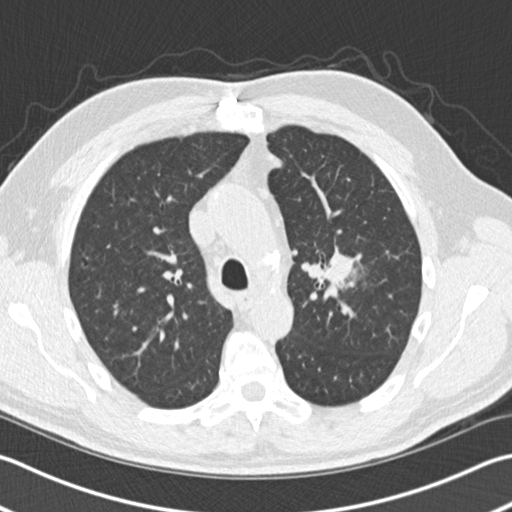
Axial slice from a low-dose chest CT screening exam. Third annual screen. Lung window (W 1500 / L -600 HU). 2 mm slice thickness. Standard (soft-tissue) reconstruction kernel (B30f). Slice 47 of 153 in the series. 512 × 512 image matrix, field of view 346 × 346 mm. Male, age 65 years at enrolment. Former smoker at enrolment.
• Lesion marked by an expert reader, box from (x=306, y=239) to (x=370, y=303) px.
• The screening reader recorded 4 non-calcified nodules or masses ≥4 mm on this exam (left upper lobe, left upper lobe, left lower lobe, right middle lobe); which of them this box marks is not recorded.
• Official screen result: positive, other.
• Participant outcome: lung cancer diagnosed 196 days after this screen — acinar cell carcinoma, left upper lobe, stage IA (AJCC 6th edition), 25 mm at pathology.